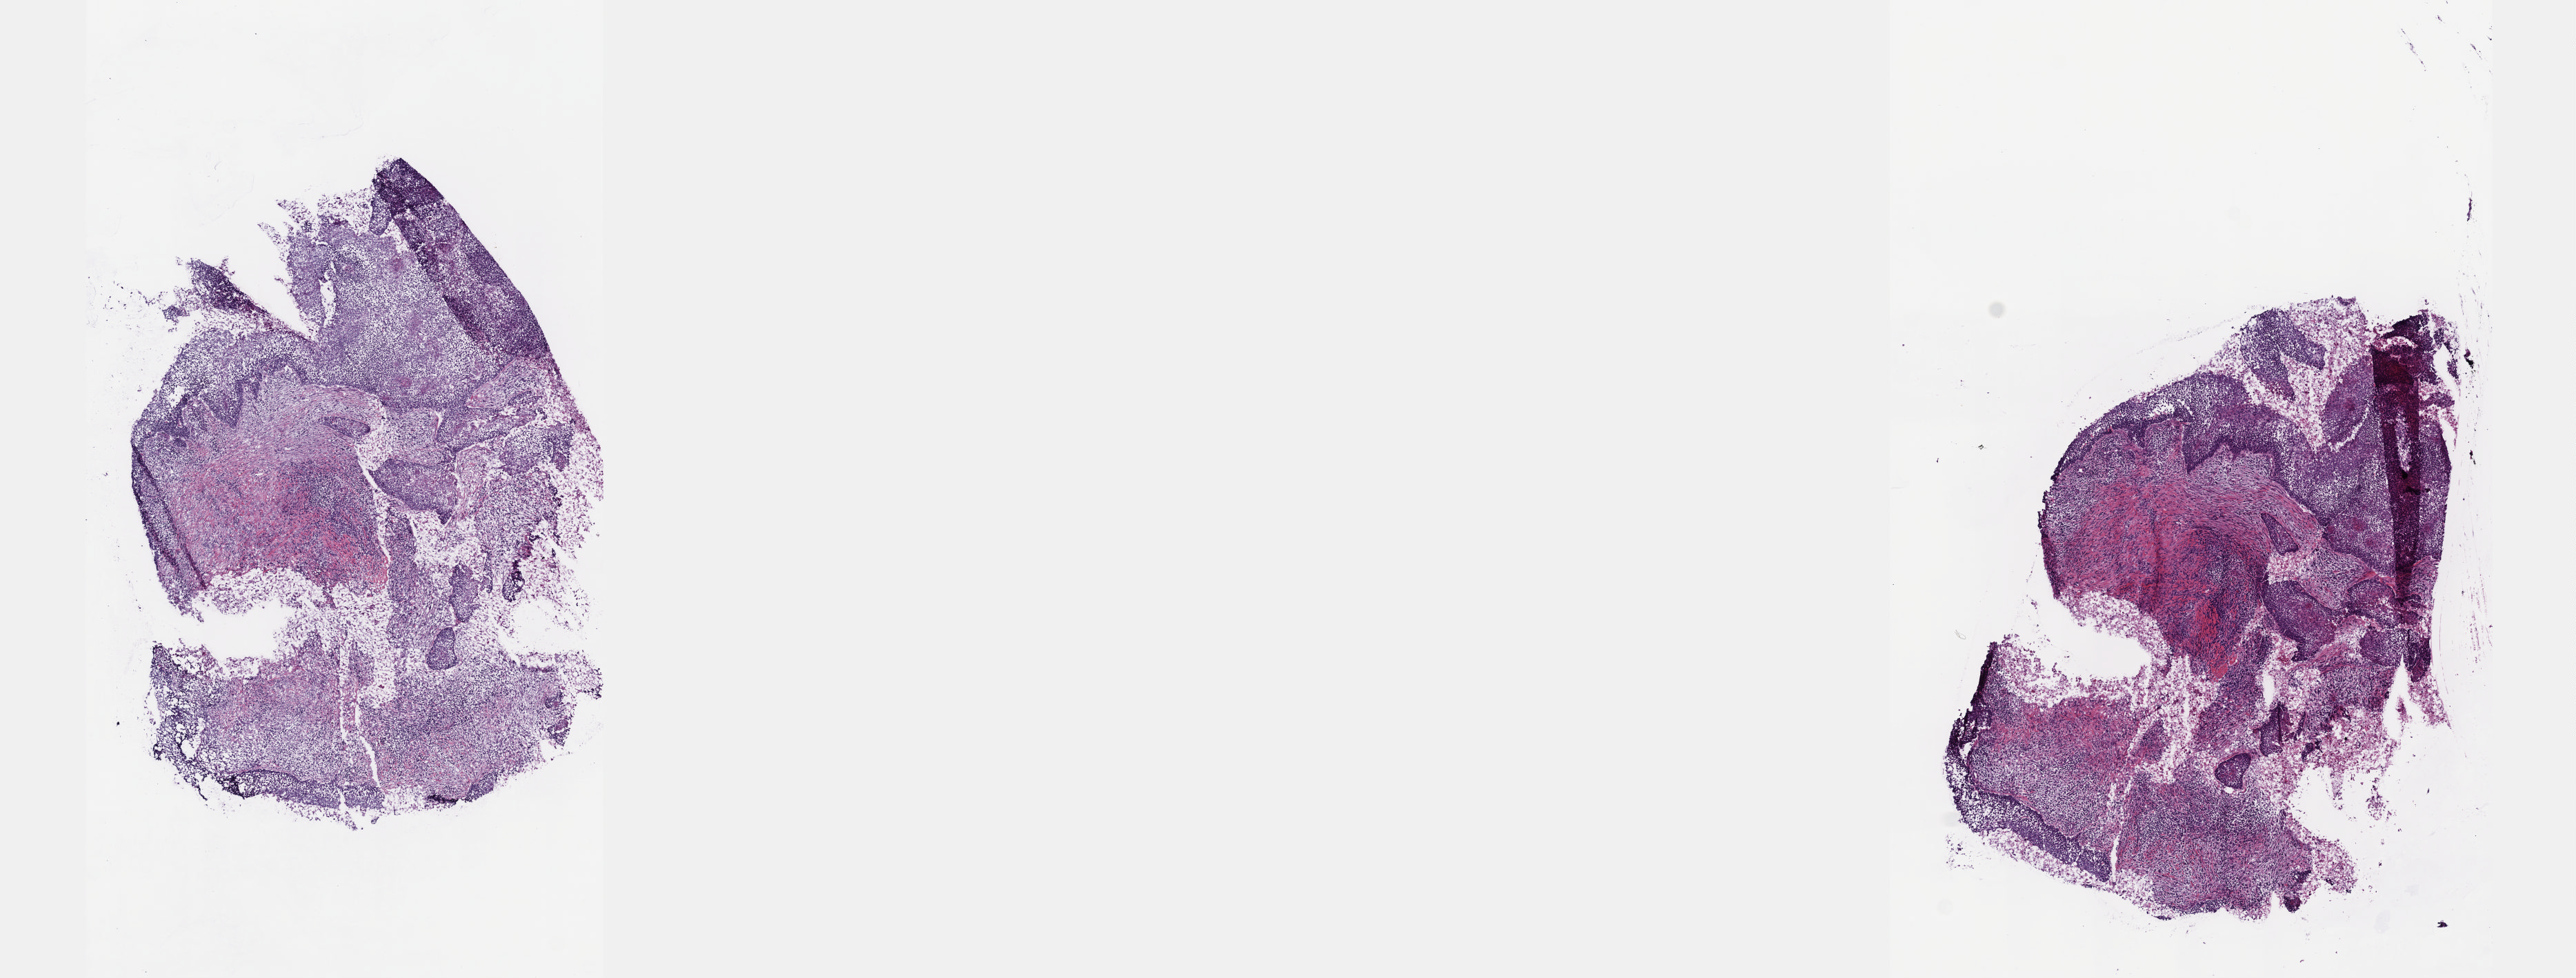
H&E whole-slide image — a low-resolution overview of the entire scanned area, about 15.1 x 5.7 mm (slide scanned at 40x); frozen section from the top of the tissue portion; sample: primary tumour, head and neck. Male patient; age at initial diagnosis 57 years. Histologic grade: G2 (moderately differentiated). Slide review estimates, as recorded: tumour cells 60%, tumour nuclei 70%, normal cells 0%, stromal cells 40%, necrosis 0%. Infiltration values recorded for this section: lymphocyte infiltration 0%, monocyte infiltration 0%, neutrophil infiltration 0%.
Histologic diagnosis: Squamous cell carcinoma, keratinizing, NOS (tonsil, NOS).